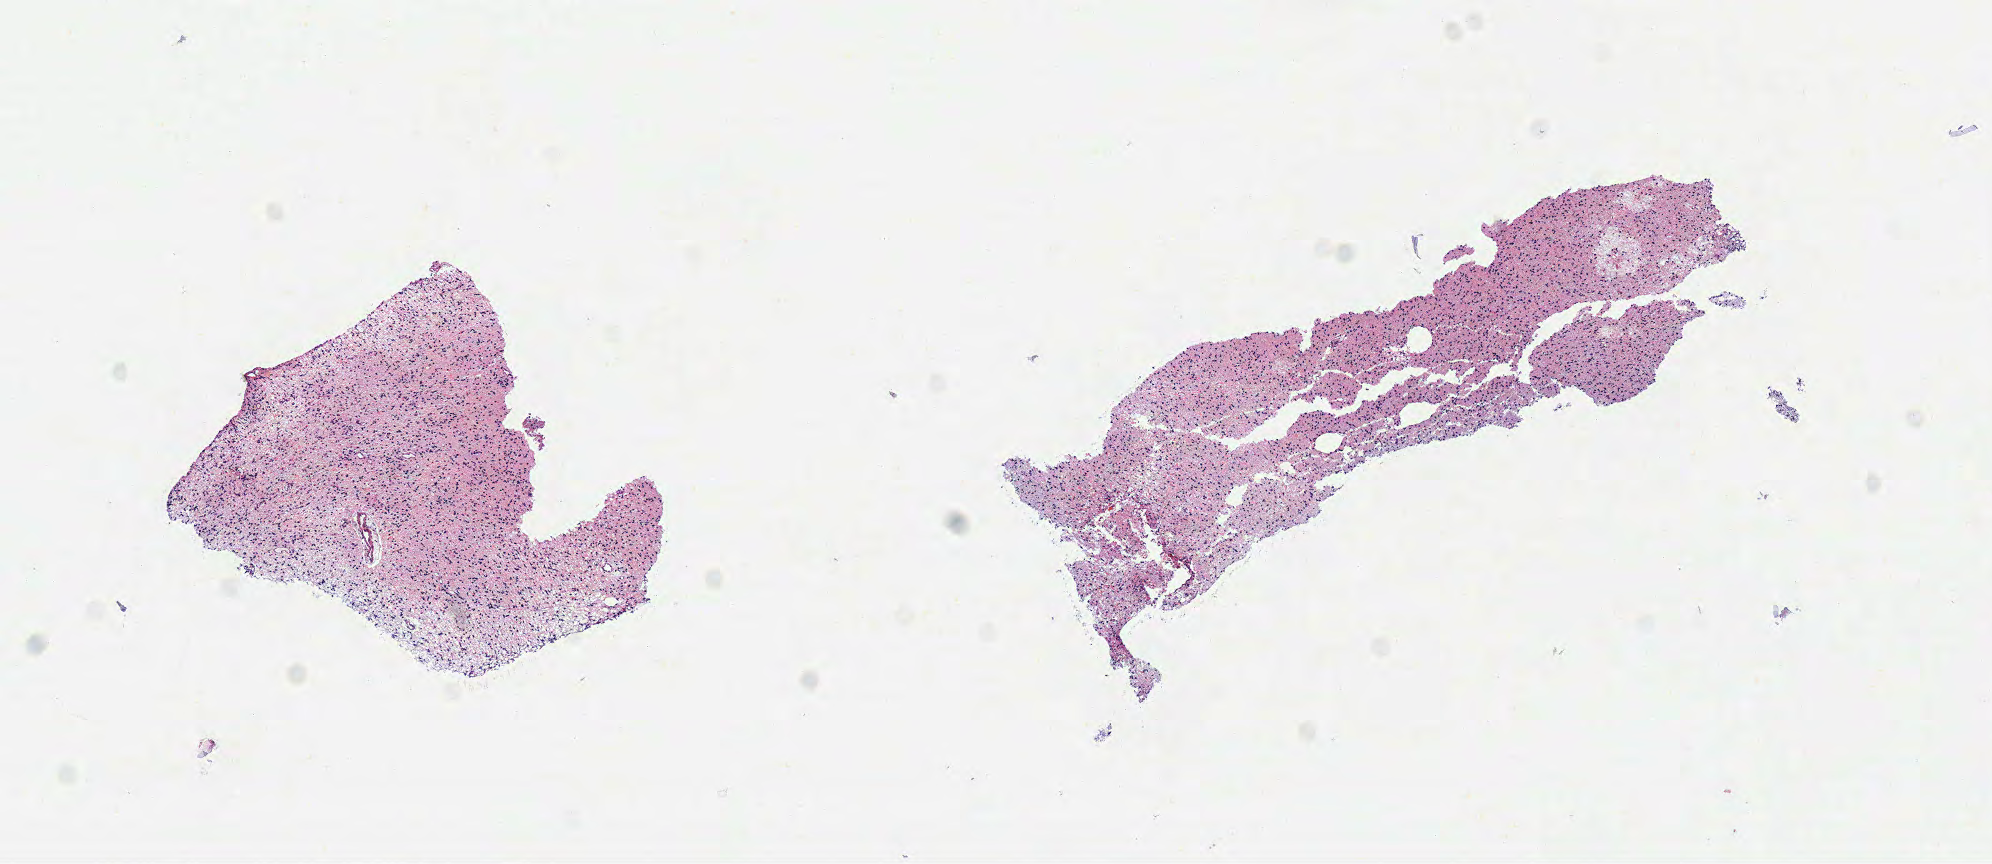
Digitized Hematoxylin and eosin (H&E) stained tissue section (whole slide) — whole scanned area (about 7.8 x 3.4 mm) shown as a low-resolution overview. Frozen section from the top of the tissue portion. Brain, primary tumour sample. Male patient; age at initial diagnosis 54 years.
Diagnosis: Oligodendroglioma, NOS.